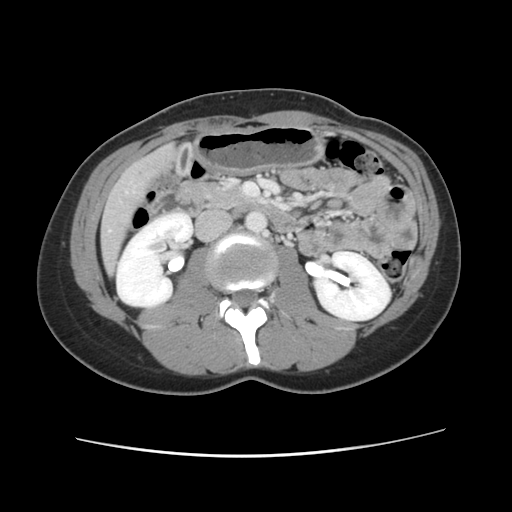
Contrast-enhanced abdominal CT, one axial slice. 120 kVp. Intravenous contrast given. Soft-tissue window (W 400 / L 40 HU). 512 × 512 image matrix, field of view 339 × 339 mm. Female patient, age 33 years. From the clinical record (not read from this slice): diagnosis: colorectal cancer liver metastases, imaged before liver resection; multiple liver metastases: yes; largest metastasis: 4.5 cm.
Structures marked on this image (expert manual segmentation):
- liver: bounding box (x1, y1, x2, y2) in pixels: (101, 147, 175, 274)
- planned liver remnant (the part of the liver to remain after resection): (102, 244, 117, 275)